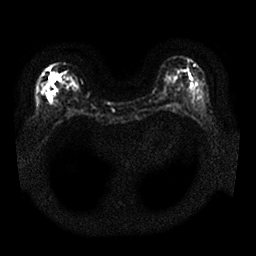
Breast MRI, one axial slice; position 8 of 25 along the scan axis; diffusion-weighted series; image 2 of 4 stored at this slice position (different b-values; order by instance number); 1.5 T; 256 × 256 image matrix. Female patient.
Outlined on this slice (manually delineated by an expert):
- tumour on diffusion-weighted imaging: box from (x=48, y=72) to (x=55, y=85) px